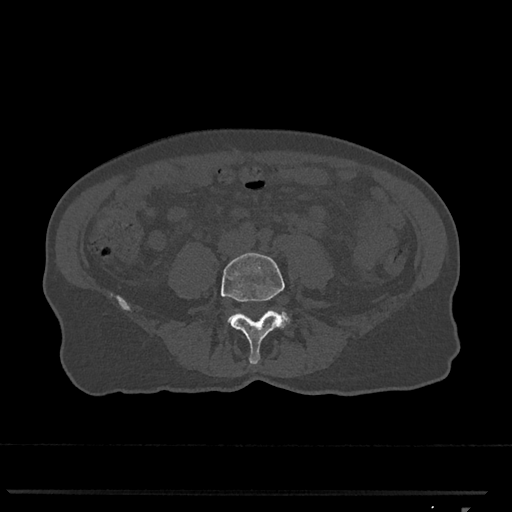
CT including the spine, one axial slice; position 199 of 793 along the scan axis; reconstruction kernel Br40s/3; bone window (W 1800 / L 400 HU); 0.5 mm slice thickness; 512 × 512 image matrix. Patient: female, 62 years. From the clinical record (not read from this slice): primary cancer: renal.
Annotated regions visible in this slice (semi-automatic segmentation, software-assisted and operator-edited):
- L4 vertebra: bounding box (x1, y1, x2, y2) in pixels: (221, 253, 285, 365)
- L5 vertebra: (227, 312, 290, 323)